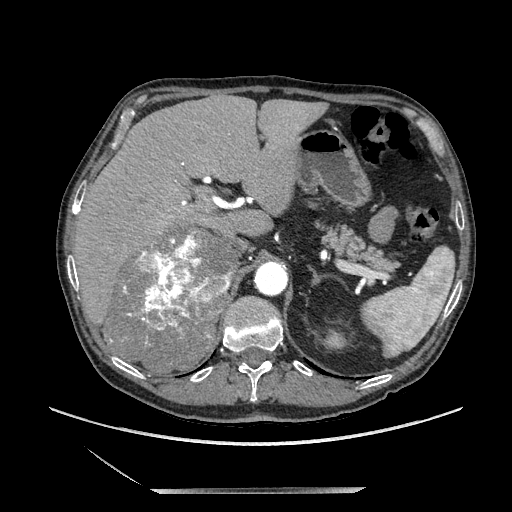
Contrast-enhanced abdominal CT, one axial slice. Slice 145 of 243 in the series (ordered by position). Soft-tissue window (W 400 / L 40 HU). 1.25 mm slice thickness. 512 × 512 image matrix, field of view 420 × 420 mm. Male patient. Case-level facts recorded for this patient, not image findings: diagnosis: adrenocortical carcinoma; tumour side: right adrenal; tumour size at pathology: 16 cm; Ki-67 index: 17 %; stage (as recorded): 3.
Structures marked on this image (semi-automatic segmentation, software-assisted and operator-edited):
- mass: bounding box <105,231,233,373> (left, top, right, bottom; pixels)